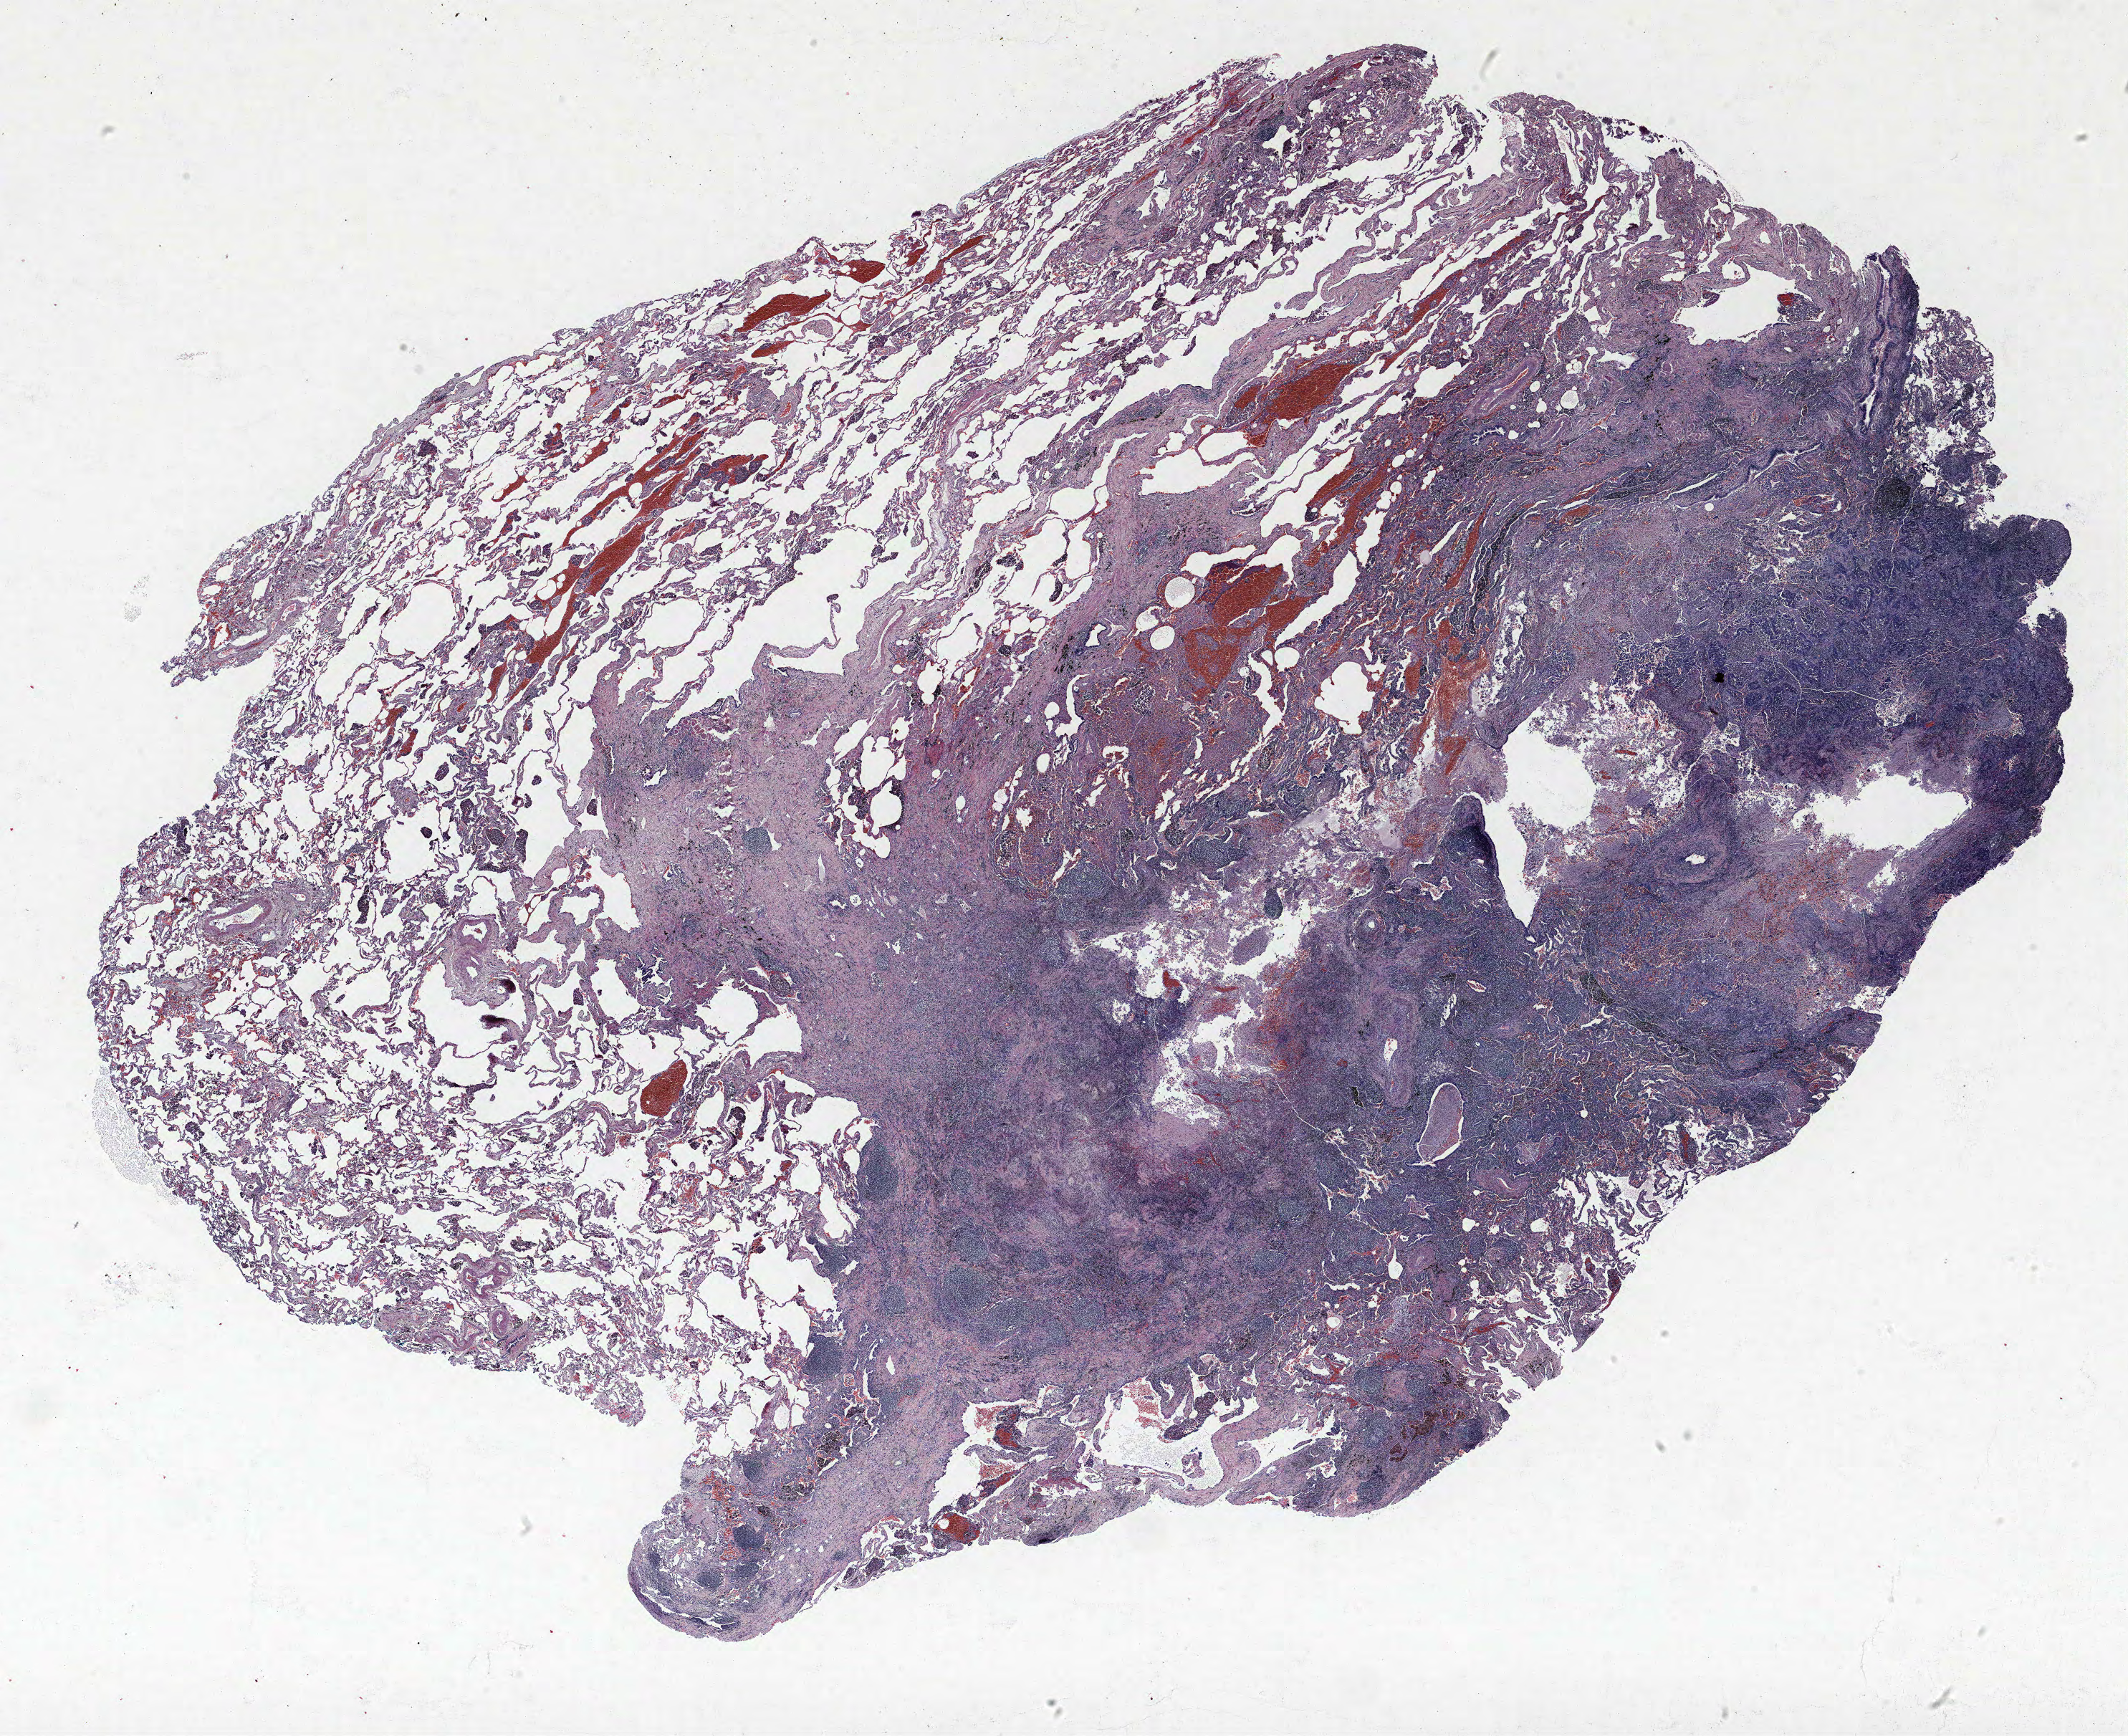
Whole-slide histology image, H&E-stained — shown as a low-resolution overview of the whole scanned area (about 23.8 x 19.4 mm, acquisition: 40x scan); formalin-fixed paraffin-embedded (FFPE) section; lung. Male, age 67 at enrolment. Grade: poorly differentiated (G3).
Primary tumour location (clinical record): right lower lobe. Tumour size (pathology): 25 mm. Participant's lung-cancer diagnosis: Adenocarcinoma, NOS (ICD-O-3 8140/3). Stage (AJCC 6th edition): IA.